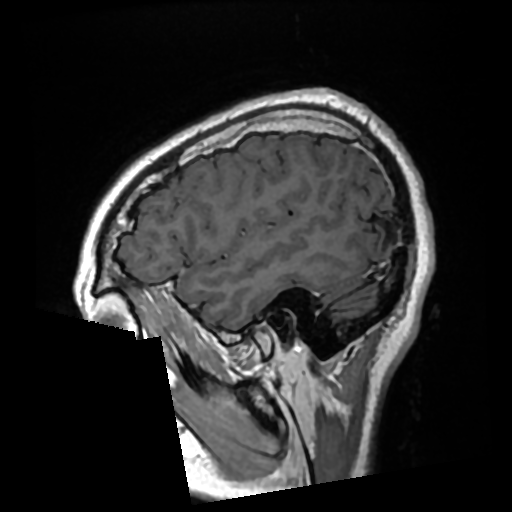
Brain MRI from a brain-tumour surgery series, one sagittal slice; slice 72 of 276 in the series (ordered by position); T1-weighted post-contrast; 512 × 512 image matrix. Case-level facts recorded for this patient, not image findings: histopathology: Glioma with ependymal features; WHO grade: 2; tumour location: Left Parietal.
Annotated regions visible in this slice (outlined manually by an expert reader):
- previous resection cavity: bounding box (x1, y1, x2, y2) in pixels: (379, 229, 391, 243)